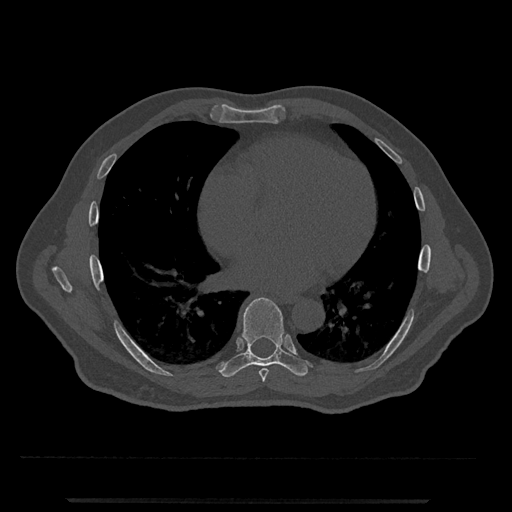
CT including the spine, one axial slice; position 641 of 797 along the scan axis; reconstruction kernel Br40s/3; 120 kVp; bone window (W 1800 / L 400 HU); 0.5 mm slice thickness; 512 × 512 image matrix. Patient: male, 63 years. From the clinical record (not read from this slice): primary cancer: prostate.
Outlined on this slice (semi-automatically segmented with operator editing):
- T7 vertebra: bounding box (x1, y1, x2, y2) in pixels: (259, 368, 268, 382)
- T8 vertebra: (220, 297, 311, 377)